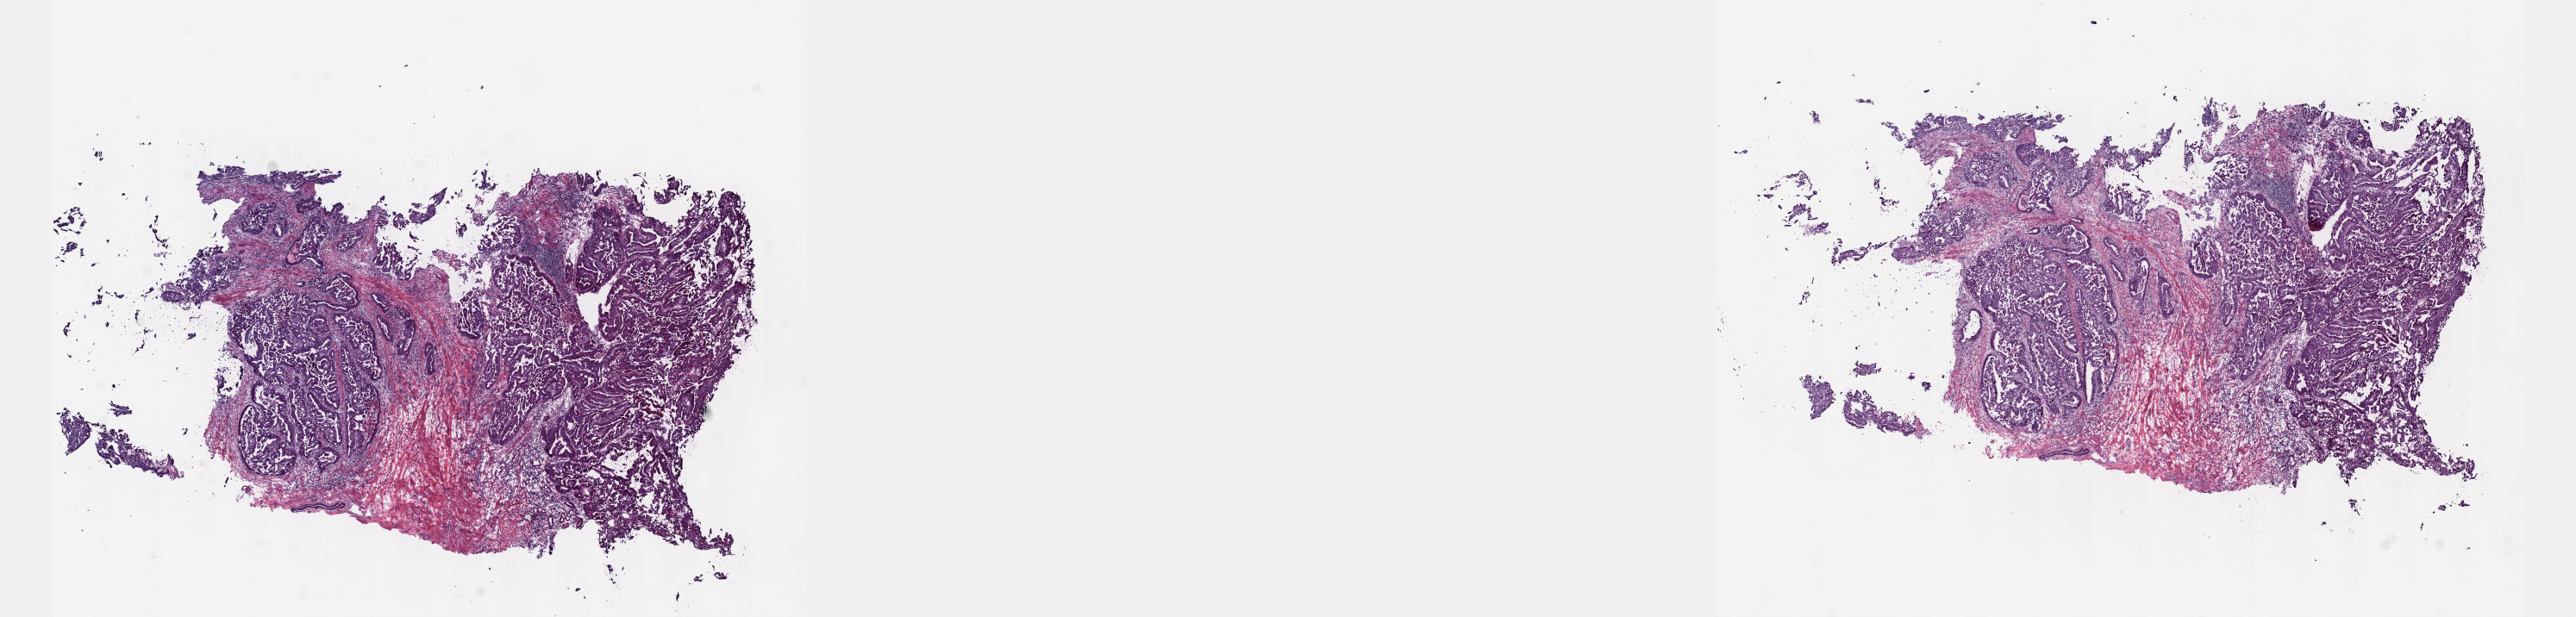
Whole-slide histology image, H&E-stained — whole scanned area (about 24.1 x 5.8 mm, acquisition: 40x scan) shown as a low-resolution overview, frozen section, esophagus, primary tumour sample. Male, age 77 years at initial diagnosis. Histologic grade: GX (grade cannot be assessed). Slide review estimates, as recorded: tumour cells 85%, tumour nuclei 60%, normal cells 15%, stromal cells 0%, necrosis 0%. Inflammatory infiltration, as recorded: lymphocyte infiltration 0%, monocyte infiltration 0%, neutrophil infiltration 0%.
TNM: T3 N1 M0. Histologic diagnosis: Adenocarcinoma, NOS. AJCC pathologic stage: III (5th edition).